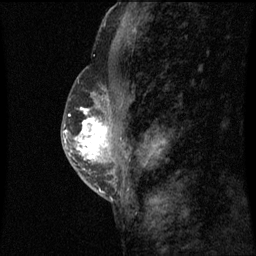
Breast MRI (dynamic contrast-enhanced), one sagittal slice. Dynamic contrast-enhanced series, image 2 of 3 at this slice position (ordered by acquisition). 1.5 T. TE 4.2 ms, TR 8.9 ms. 2 mm slice thickness. 256 × 256 image matrix, field of view 200 × 200 mm. Female patient, age 50 years. Case-level facts recorded for this patient, not image findings: setting: breast cancer imaged before/during neoadjuvant chemotherapy; receptor status: triple-negative.
Structures marked on this image (semi-automatic segmentation, software-assisted and operator-edited):
- analysis volume of interest (the breast-tissue region the enhancement analysis was run in; not a lesion): bounding box (x1, y1, x2, y2) in pixels: (68, 80, 111, 169)
- tumour enhancement mask (voxels above the 70 % enhancement threshold inside the analysis volume of interest): (77, 110, 109, 159)